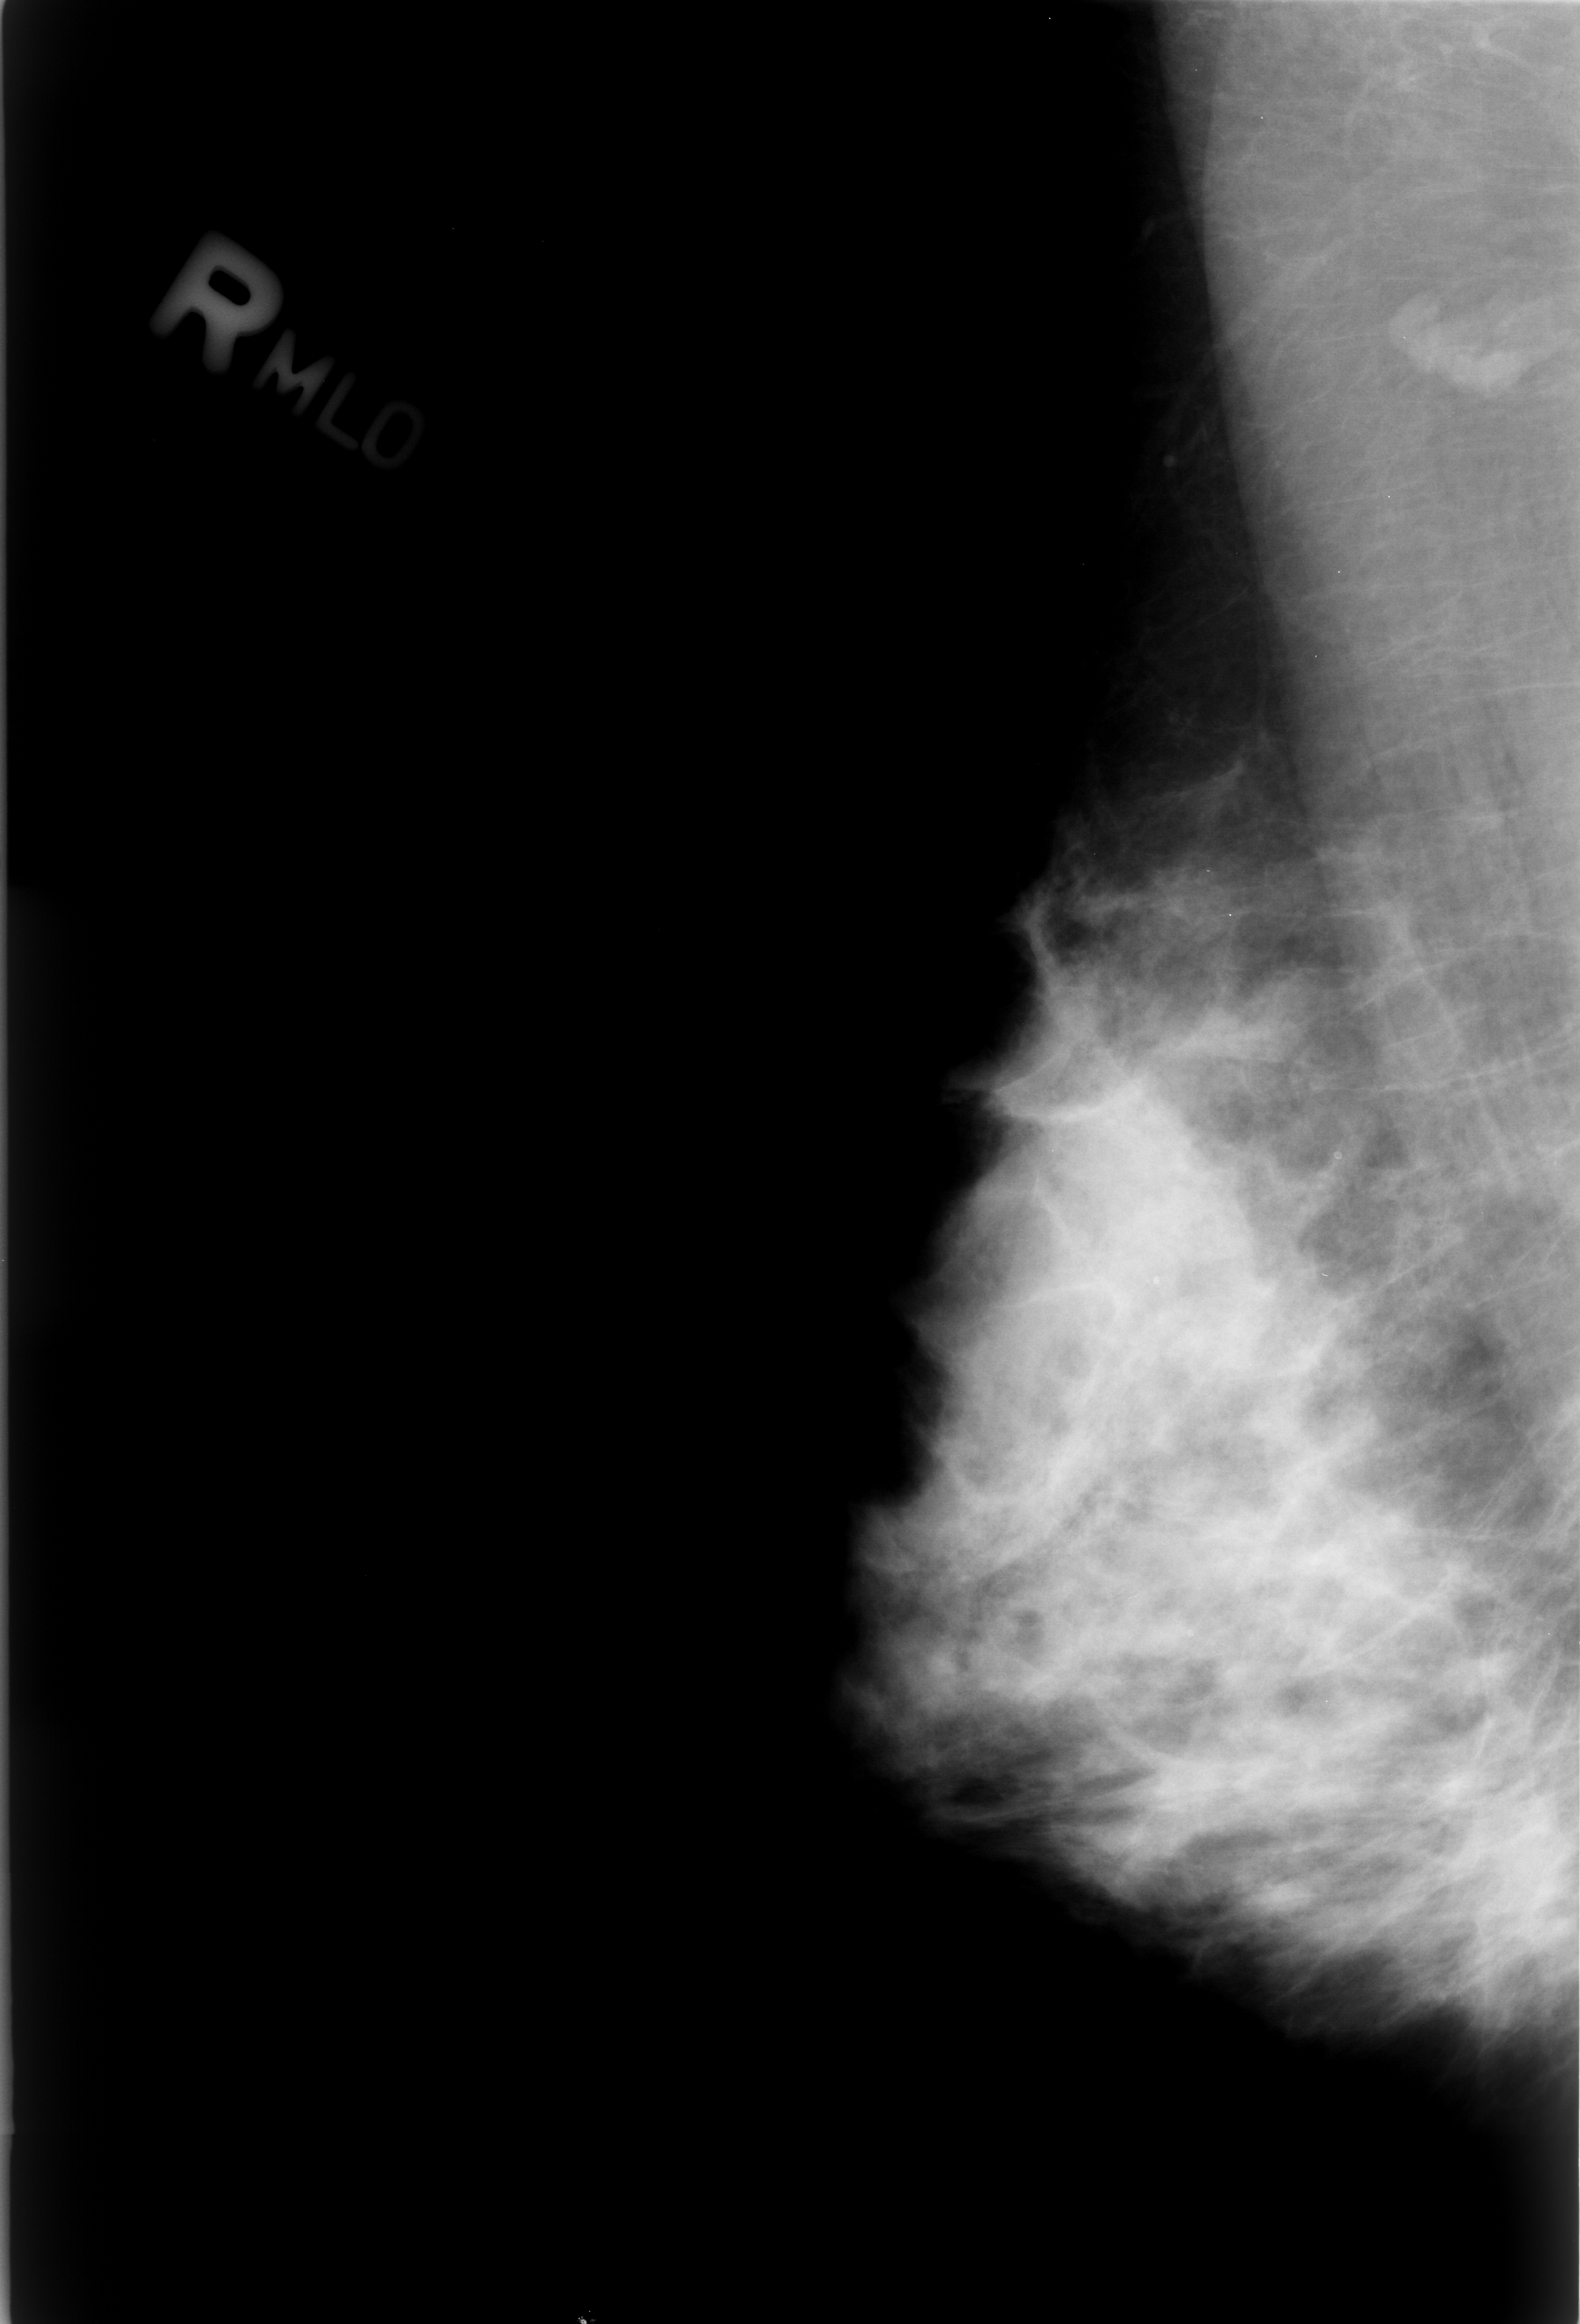
Scanned film-screen mammogram. Right breast. Mediolateral oblique (MLO) view. BI-RADS breast density category 4 (scale 1–4). 1580 × 2324 image matrix.
Expert-marked regions of interest on this film, with their recorded descriptors:
- Finding 1 of 3: calcifications, morphology lucent center; BI-RADS assessment category 2; subtlety rating 4 on a 1 (subtle) to 5 (obvious) scale; outcome (as recorded, no biopsy): benign without callback (not worked up further): bounding box [x1, y1, x2, y2] px = [1120, 1257, 1196, 1324]
- Finding 2 of 3: calcifications, morphology lucent center; BI-RADS assessment category 2; subtlety rating 4 on a 1 (subtle) to 5 (obvious) scale; benign; no additional work-up was recommended (outcome (as recorded, no biopsy): benign without callback): [1166, 1616, 1250, 1692]
- Finding 3 of 3: calcifications, morphology lucent center; BI-RADS assessment category 2; benign; no additional work-up was recommended (outcome (as recorded, no biopsy): benign without callback): [1302, 1120, 1387, 1217]